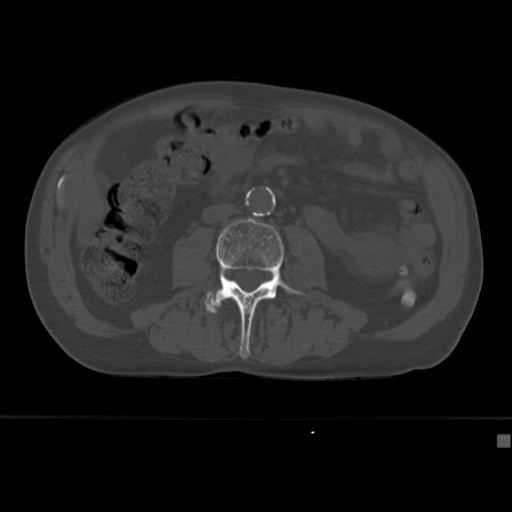
CT including the spine, one axial slice. Position 126 of 430 along the scan axis. Reconstruction kernel Br40s. 120 kVp. Bone window (W 1800 / L 400 HU). 512 × 512 image matrix, field of view 337 × 337 mm. Male patient, age 64 years. From the clinical record (not read from this slice): primary cancer: uterus; vertebrae with lytic lesions (as recorded): T1, T4, T5, T7, L5.
Annotated regions visible in this slice (semi-automatically segmented with operator editing):
- L2 vertebra: bounding box (x1, y1, x2, y2) in pixels: (270, 306, 273, 309)
- L3 vertebra: (209, 217, 304, 359)
- L4 vertebra: (204, 291, 214, 313)